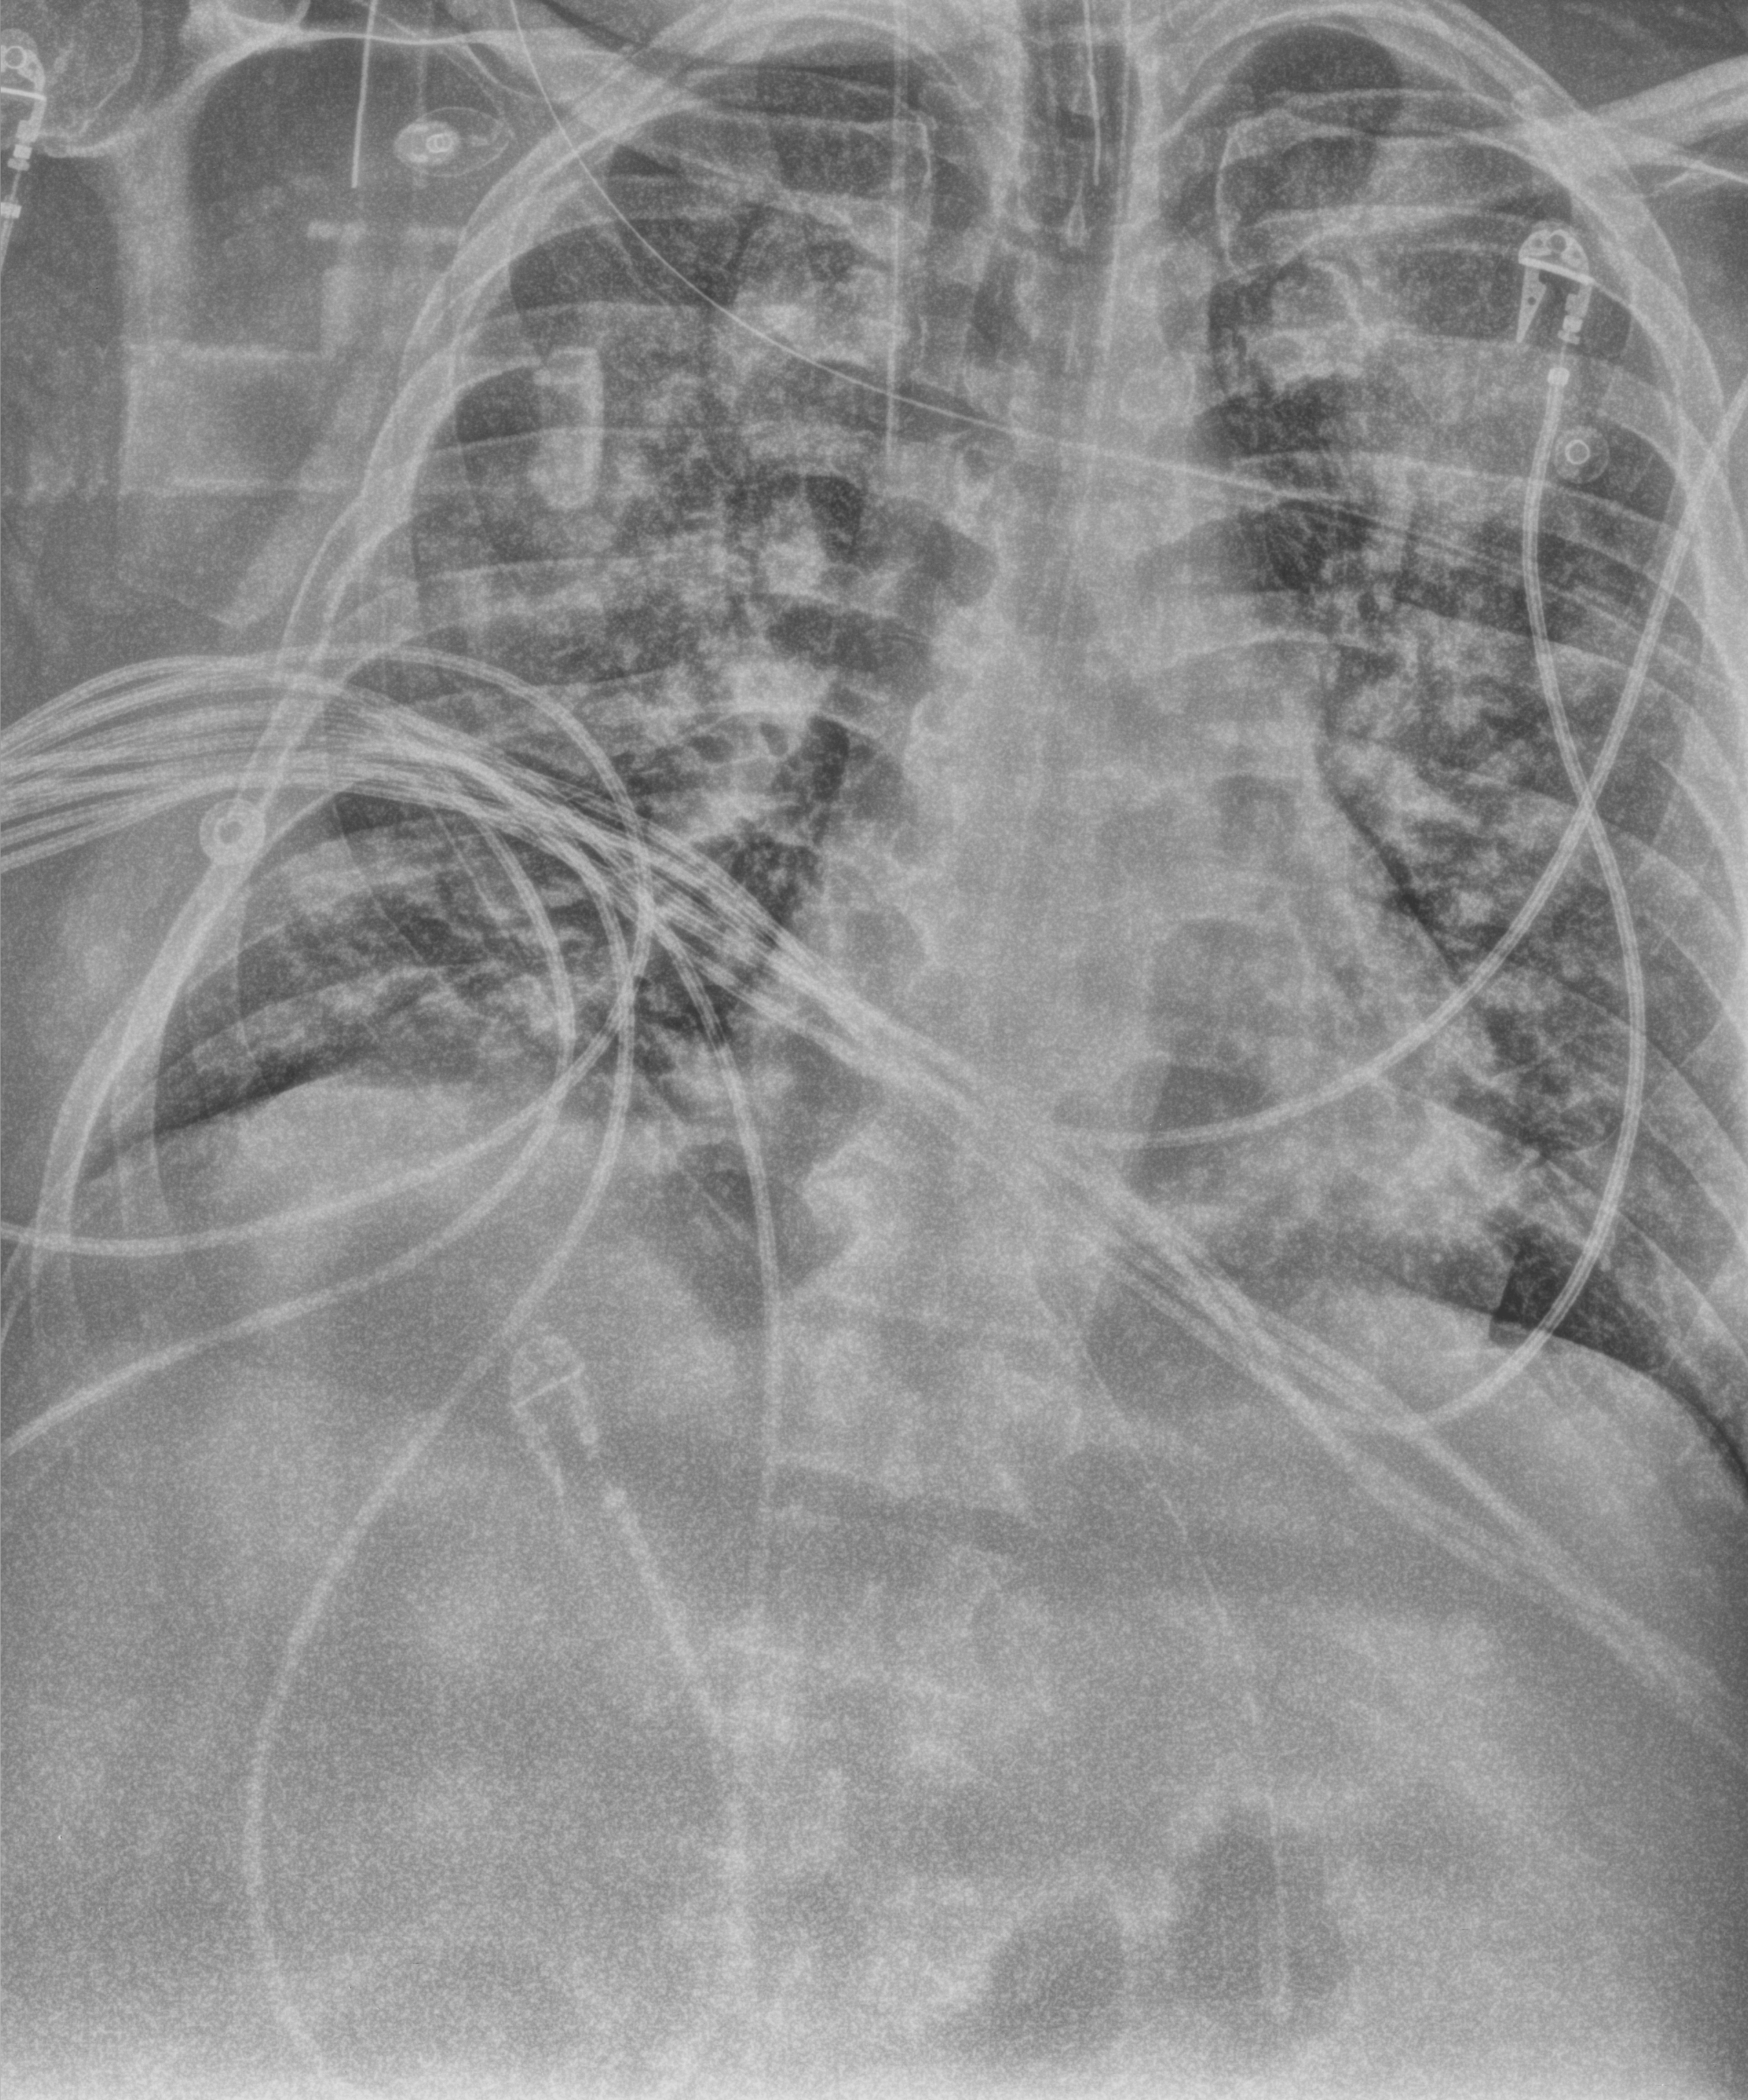
Chest X-ray (portable), anteroposterior (AP) projection. Patient hospitalised with COVID-19; male, aged 18–59 years.
Hospital-stay facts (about this admission, not read from this image; timing relative to this image not recorded): other chronic lung disease (admission record): yes; admitted to intensive care during this hospital stay: yes.